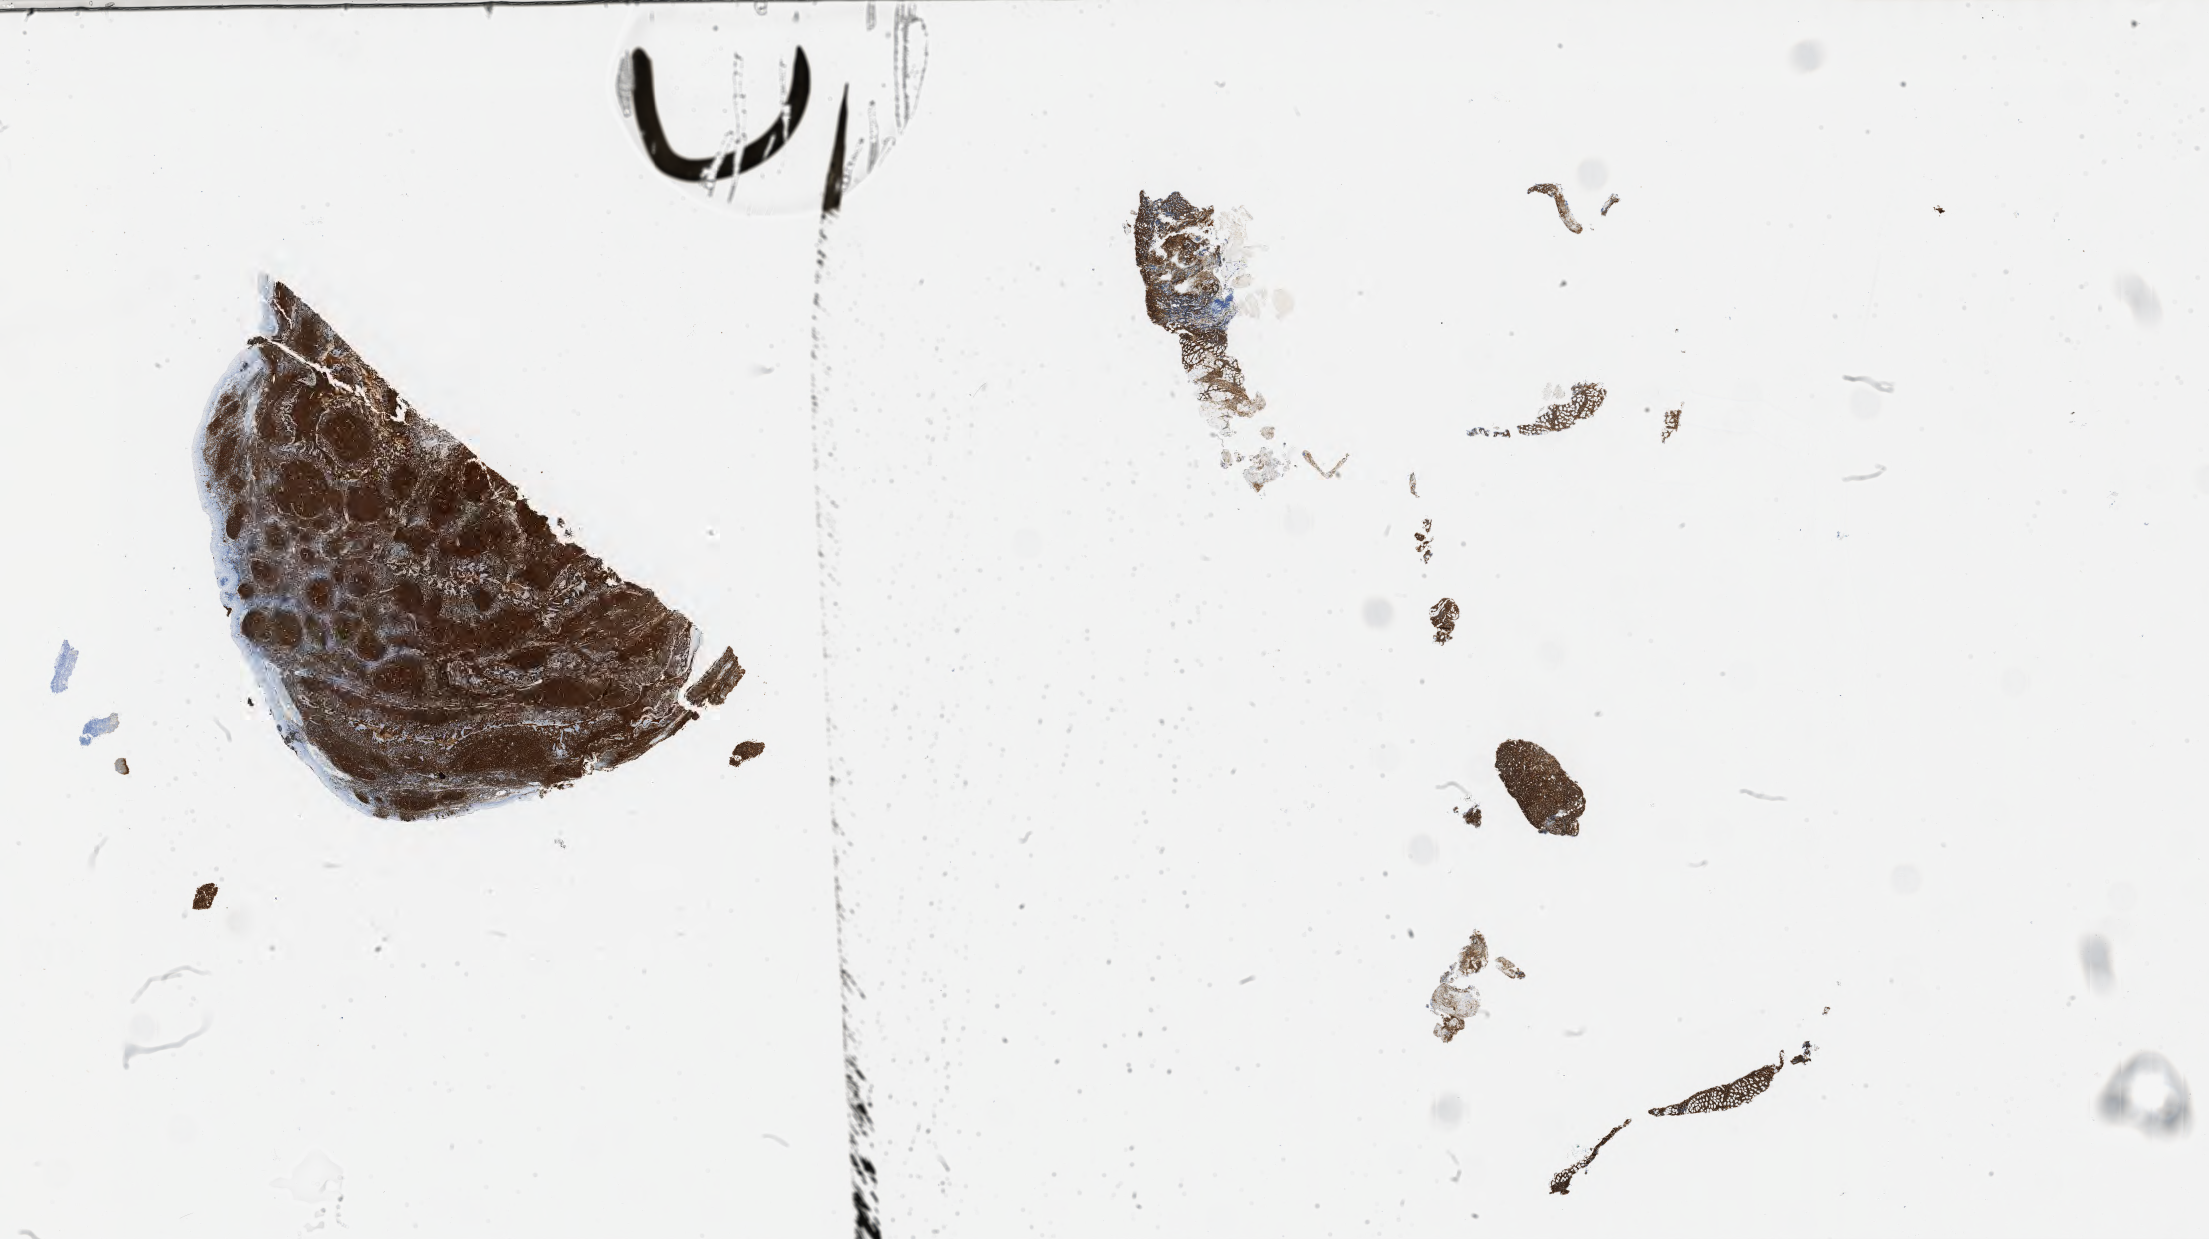
Immunohistochemistry (IHC) whole-slide image stained for CD20 — a low-resolution overview of the entire scanned area, about 35.7 x 20.0 mm, specimen: tumor tissue, site: bone of pelvis. Male patient, 53 years old.
- diagnosis: Burkitt lymphoma, NOS